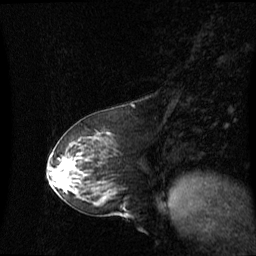
Breast MRI (dynamic contrast-enhanced), one sagittal slice; slice 26 of 60 in the series (ordered by position); dynamic contrast-enhanced series, image 2 of 3 at this slice position (ordered by acquisition); 1.5 T; TE 4.2 ms, TR 8.4 ms; 2.1 mm slice thickness; 256 × 256 image matrix. Patient: female, 59 years. From the clinical record (not read from this slice): setting: breast cancer imaged before/during neoadjuvant chemotherapy; receptor status: HR-positive, HER2-negative.
Structures marked on this image (semi-automatically segmented with operator editing):
- analysis volume of interest (the breast-tissue region the enhancement analysis was run in; not a lesion): bounding box [x1, y1, x2, y2] px = [55, 149, 85, 191]
- tumour enhancement mask (voxels above the 70 % enhancement threshold inside the analysis volume of interest): [63, 162, 75, 171]